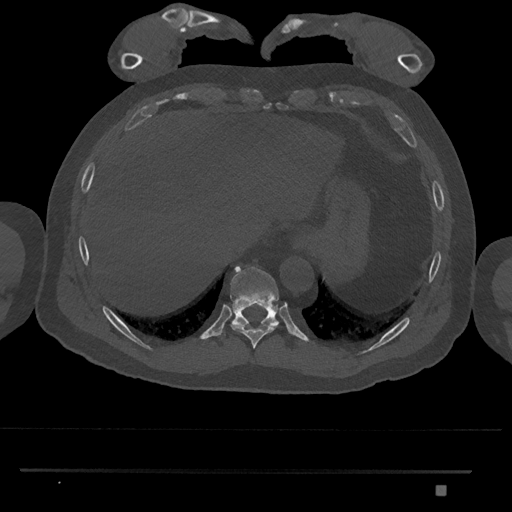
CT including the spine, one axial slice. Slice 1030 of 1134 in the series (ordered by position). Reconstruction kernel Br40s/3. 120 kVp. Bone window (W 1800 / L 400 HU). 0.5 mm slice thickness. 512 × 512 image matrix, field of view 429 × 429 mm. Male patient, age 65 years. Case-level facts recorded for this patient, not image findings: primary cancer: prostate.
Structures marked on this image (semi-automatically segmented with operator editing):
- T10 vertebra: bounding box [x1, y1, x2, y2] px = [223, 265, 279, 337]
- T9 vertebra: [231, 323, 279, 349]